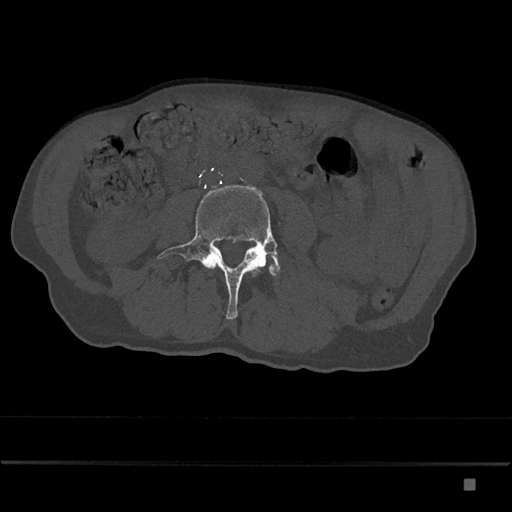
CT including the spine, one axial slice. Position 344 of 797 along the scan axis. Bone window (W 1800 / L 400 HU). 0.5 mm slice thickness. 512 × 512 image matrix. Patient: male, 72 years. From the clinical record (not read from this slice): primary cancer: prostate.
Outlined on this slice (semi-automatically segmented with operator editing):
- L4 vertebra: bounding box <157,185,280,320> (left, top, right, bottom; pixels)